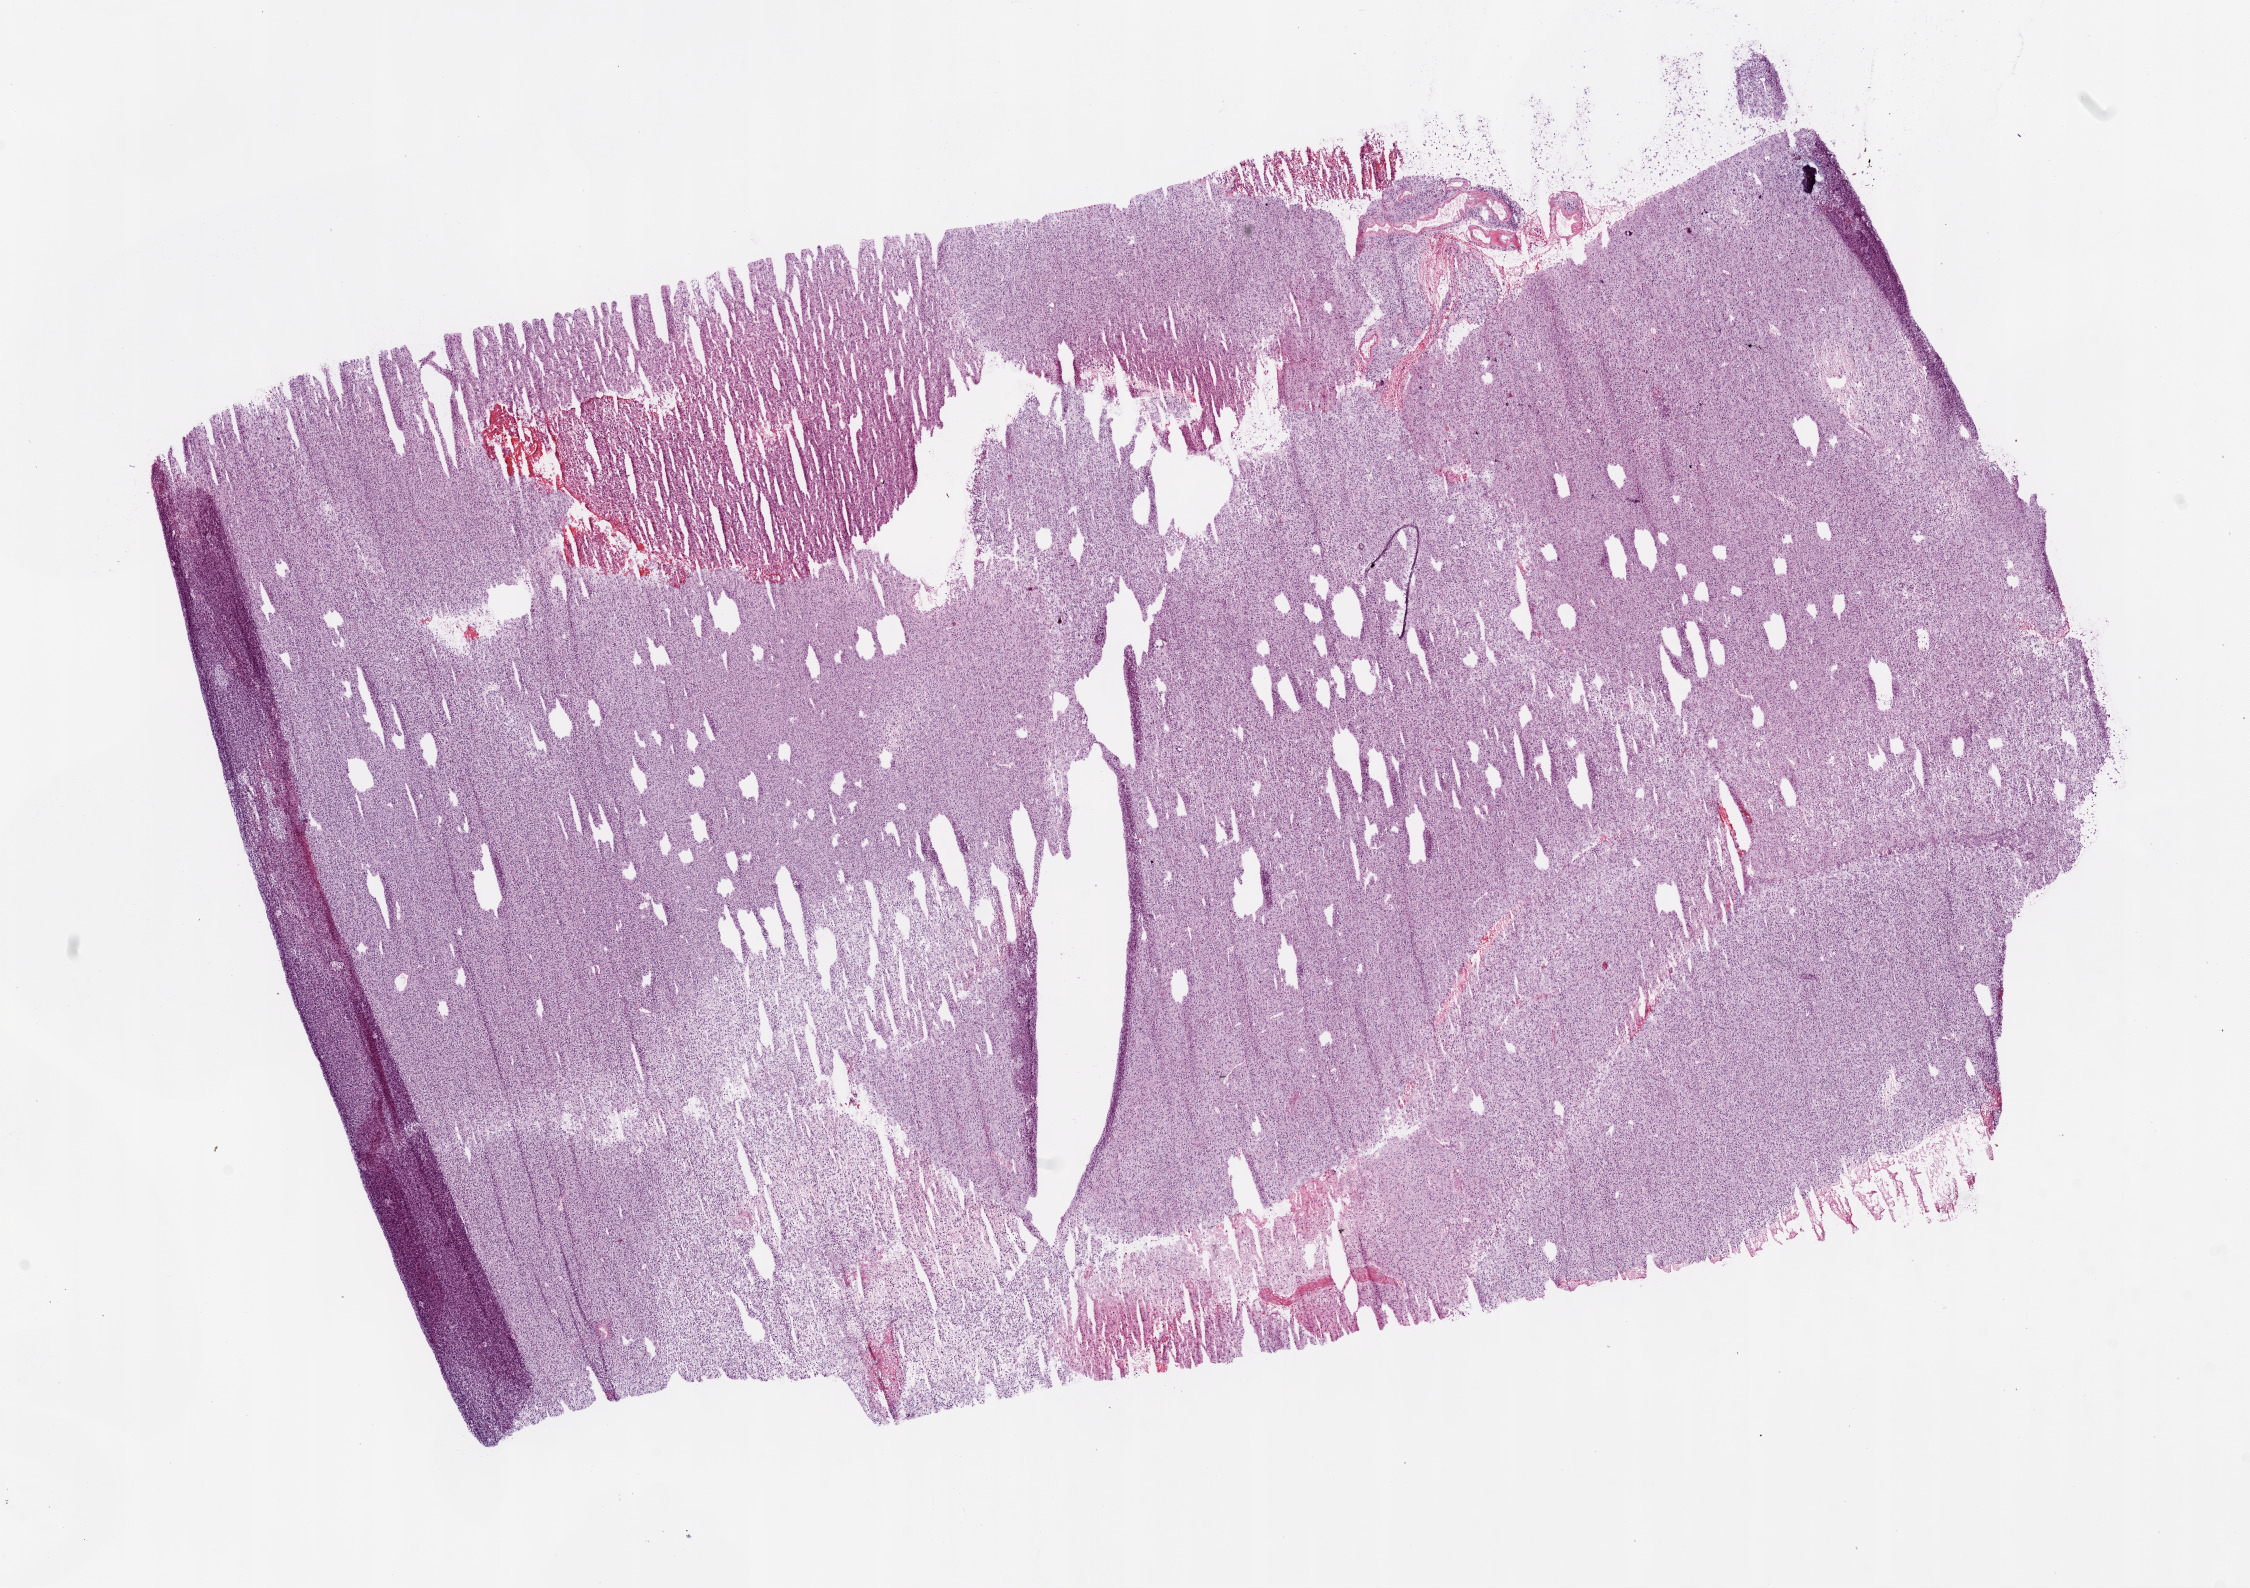
Hematoxylin and eosin (H&E) stained whole-slide image, a low-resolution overview of the entire scanned area, about 18.1 x 12.7 mm (slide scanned at 20x), frozen section from the bottom of the tissue portion, sample: primary tumour, brain. Male, age 59 years at initial diagnosis. Slide review estimates, as recorded: tumour cells 98%, tumour nuclei 85%, normal cells 0%, stromal cells 0%, necrosis 2%.
Diagnosis: Glioblastoma.